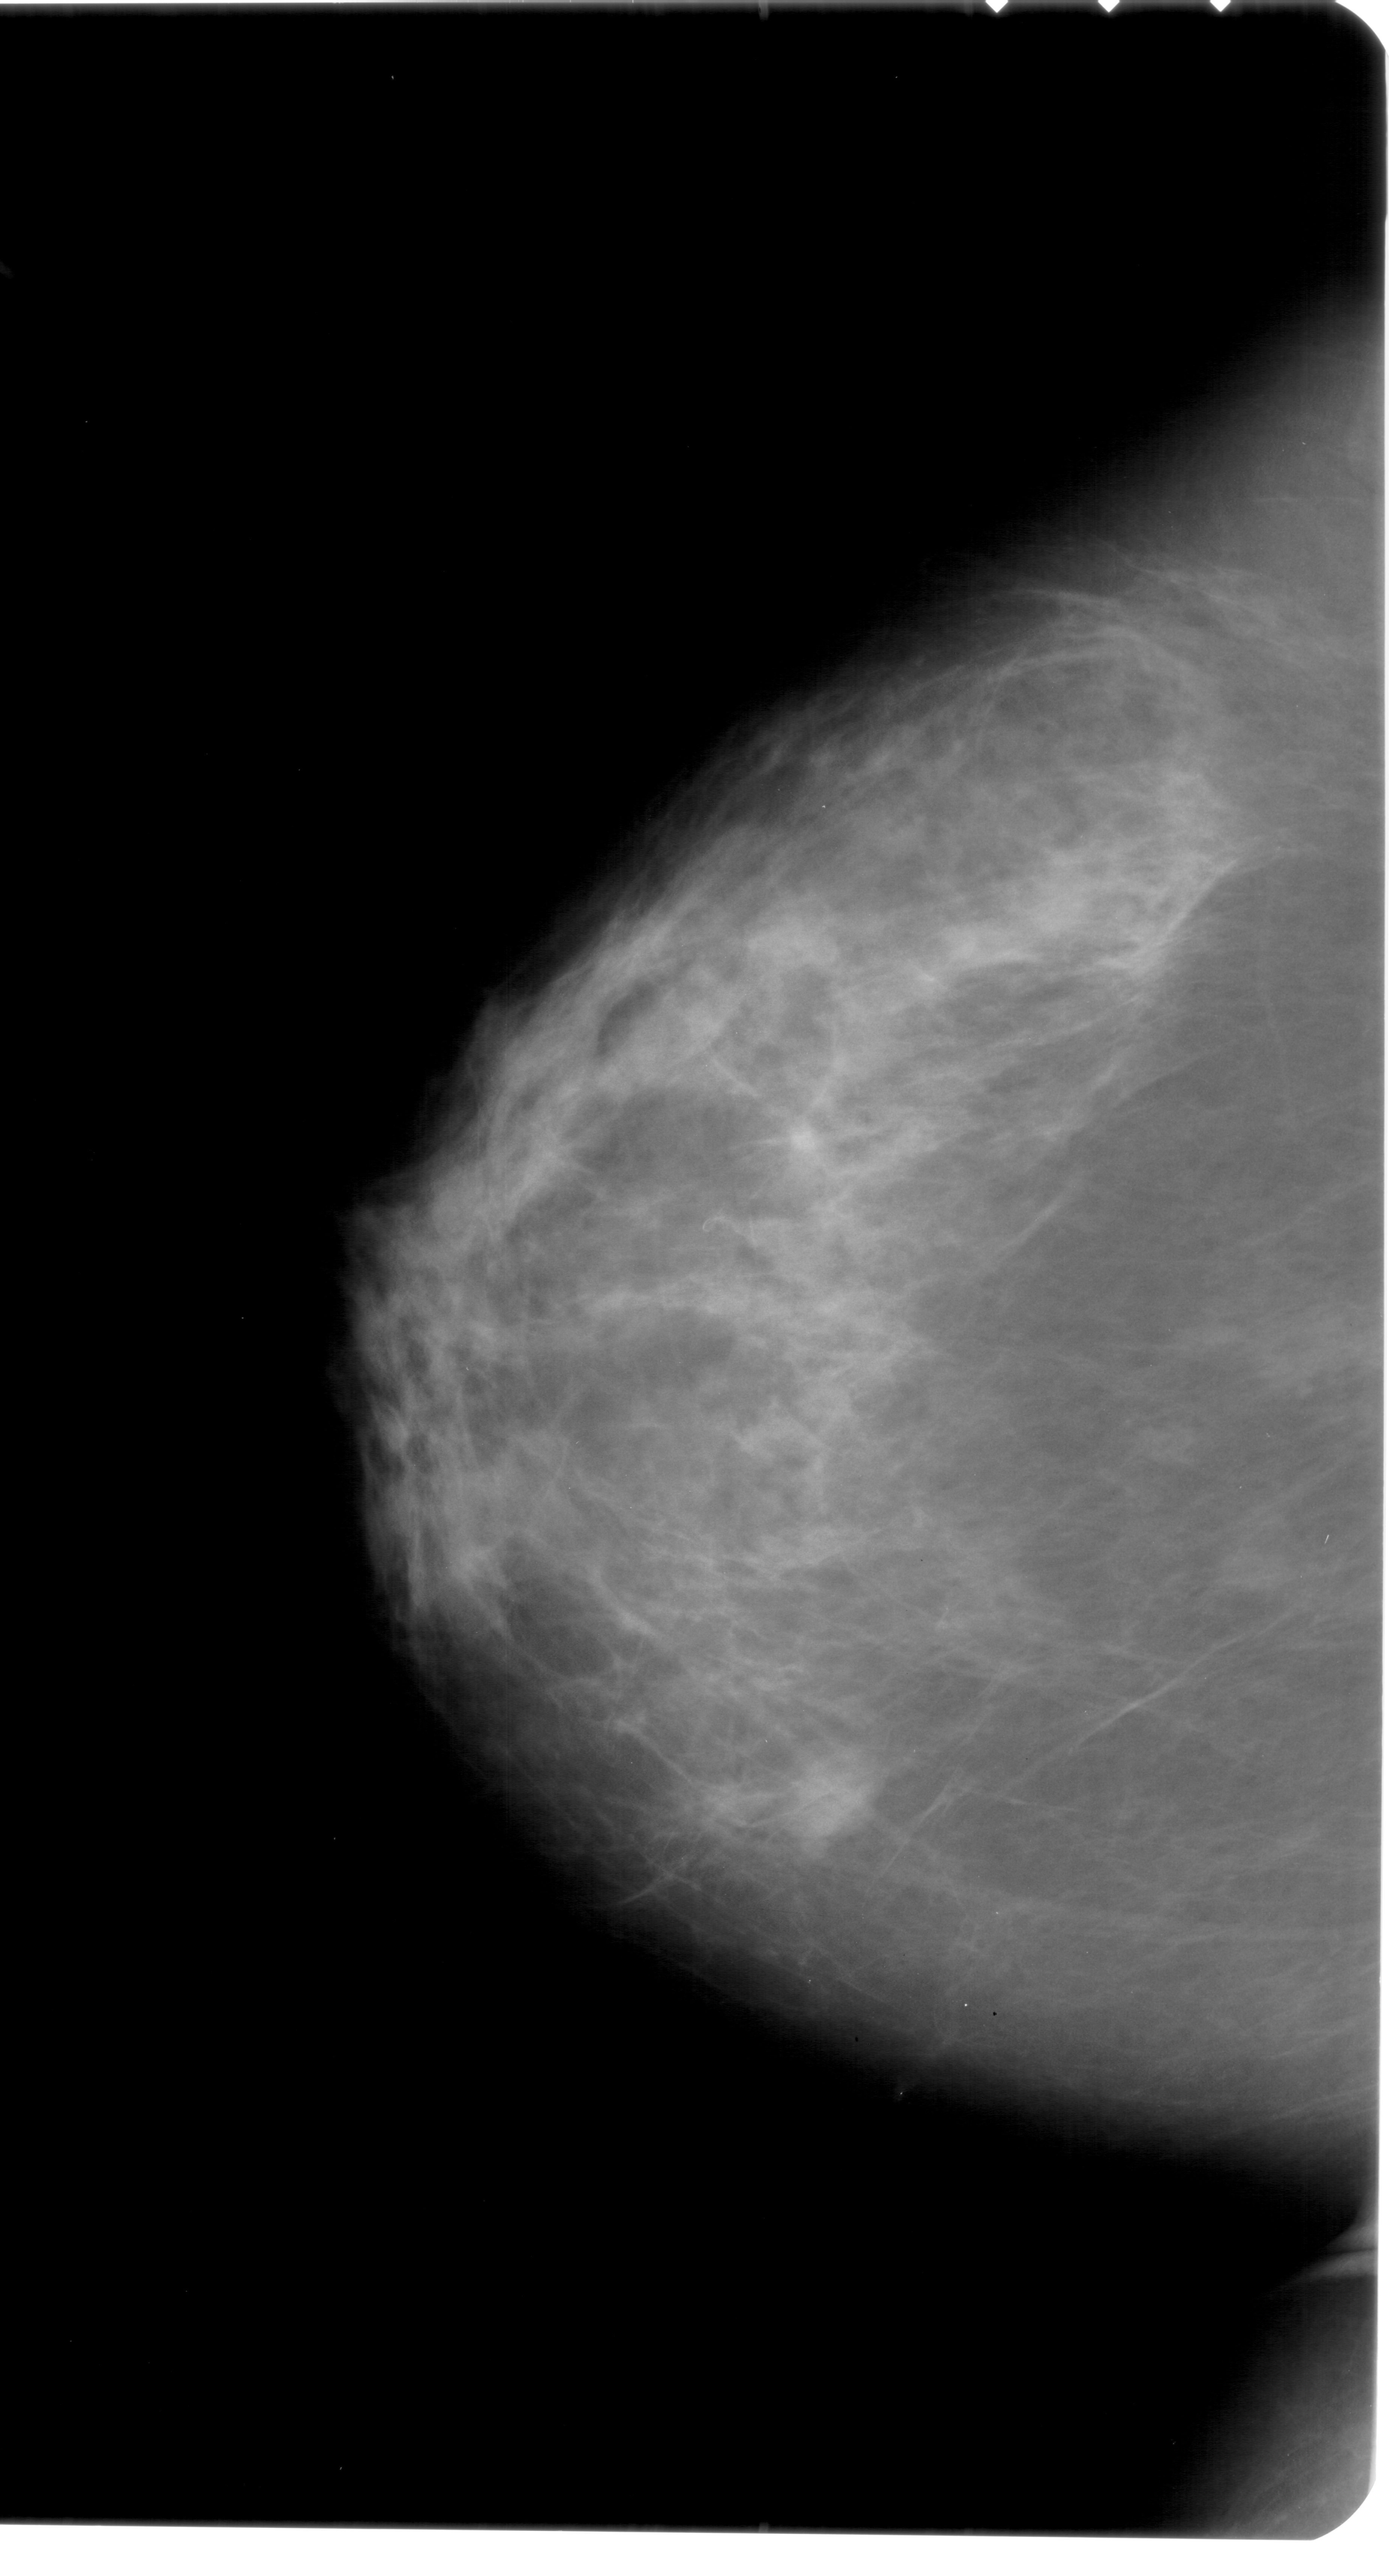
Scanned film-screen mammogram; left breast; CC view; breast composition: heterogeneously dense (BI-RADS density category 3 of 4); 1389 × 2576 image matrix.
Marked abnormalities (boxes around the expert regions of interest):
- mass, shape lobulated, margins obscured; BI-RADS assessment category 4; subtlety rating 3 on a 1 (subtle) to 5 (obvious) scale; pathology (as recorded): benign: bounding box (x1, y1, x2, y2) in pixels: (785, 1750, 885, 1849)